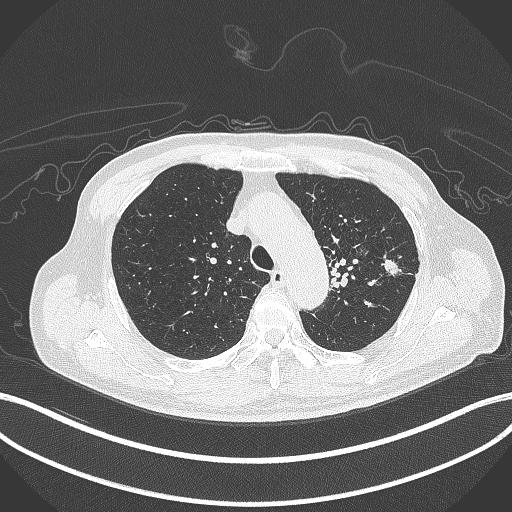
Chest CT, one axial slice. Position 332 of 417 along the scan axis. Reconstruction kernel B70f. 120 kVp. Lung window (W 1500 / L -600 HU). 512 × 512 image matrix, field of view 400 × 400 mm. Male patient, age 77 years. Case-level facts recorded for this patient, not image findings: clinical TNM (as recorded): T3 N1 M0.
Structures marked on this image (bounding box drawn by a radiologist):
- lung tumour (recorded histology: adenocarcinoma): bounding box [x1, y1, x2, y2] px = [380, 253, 405, 281]